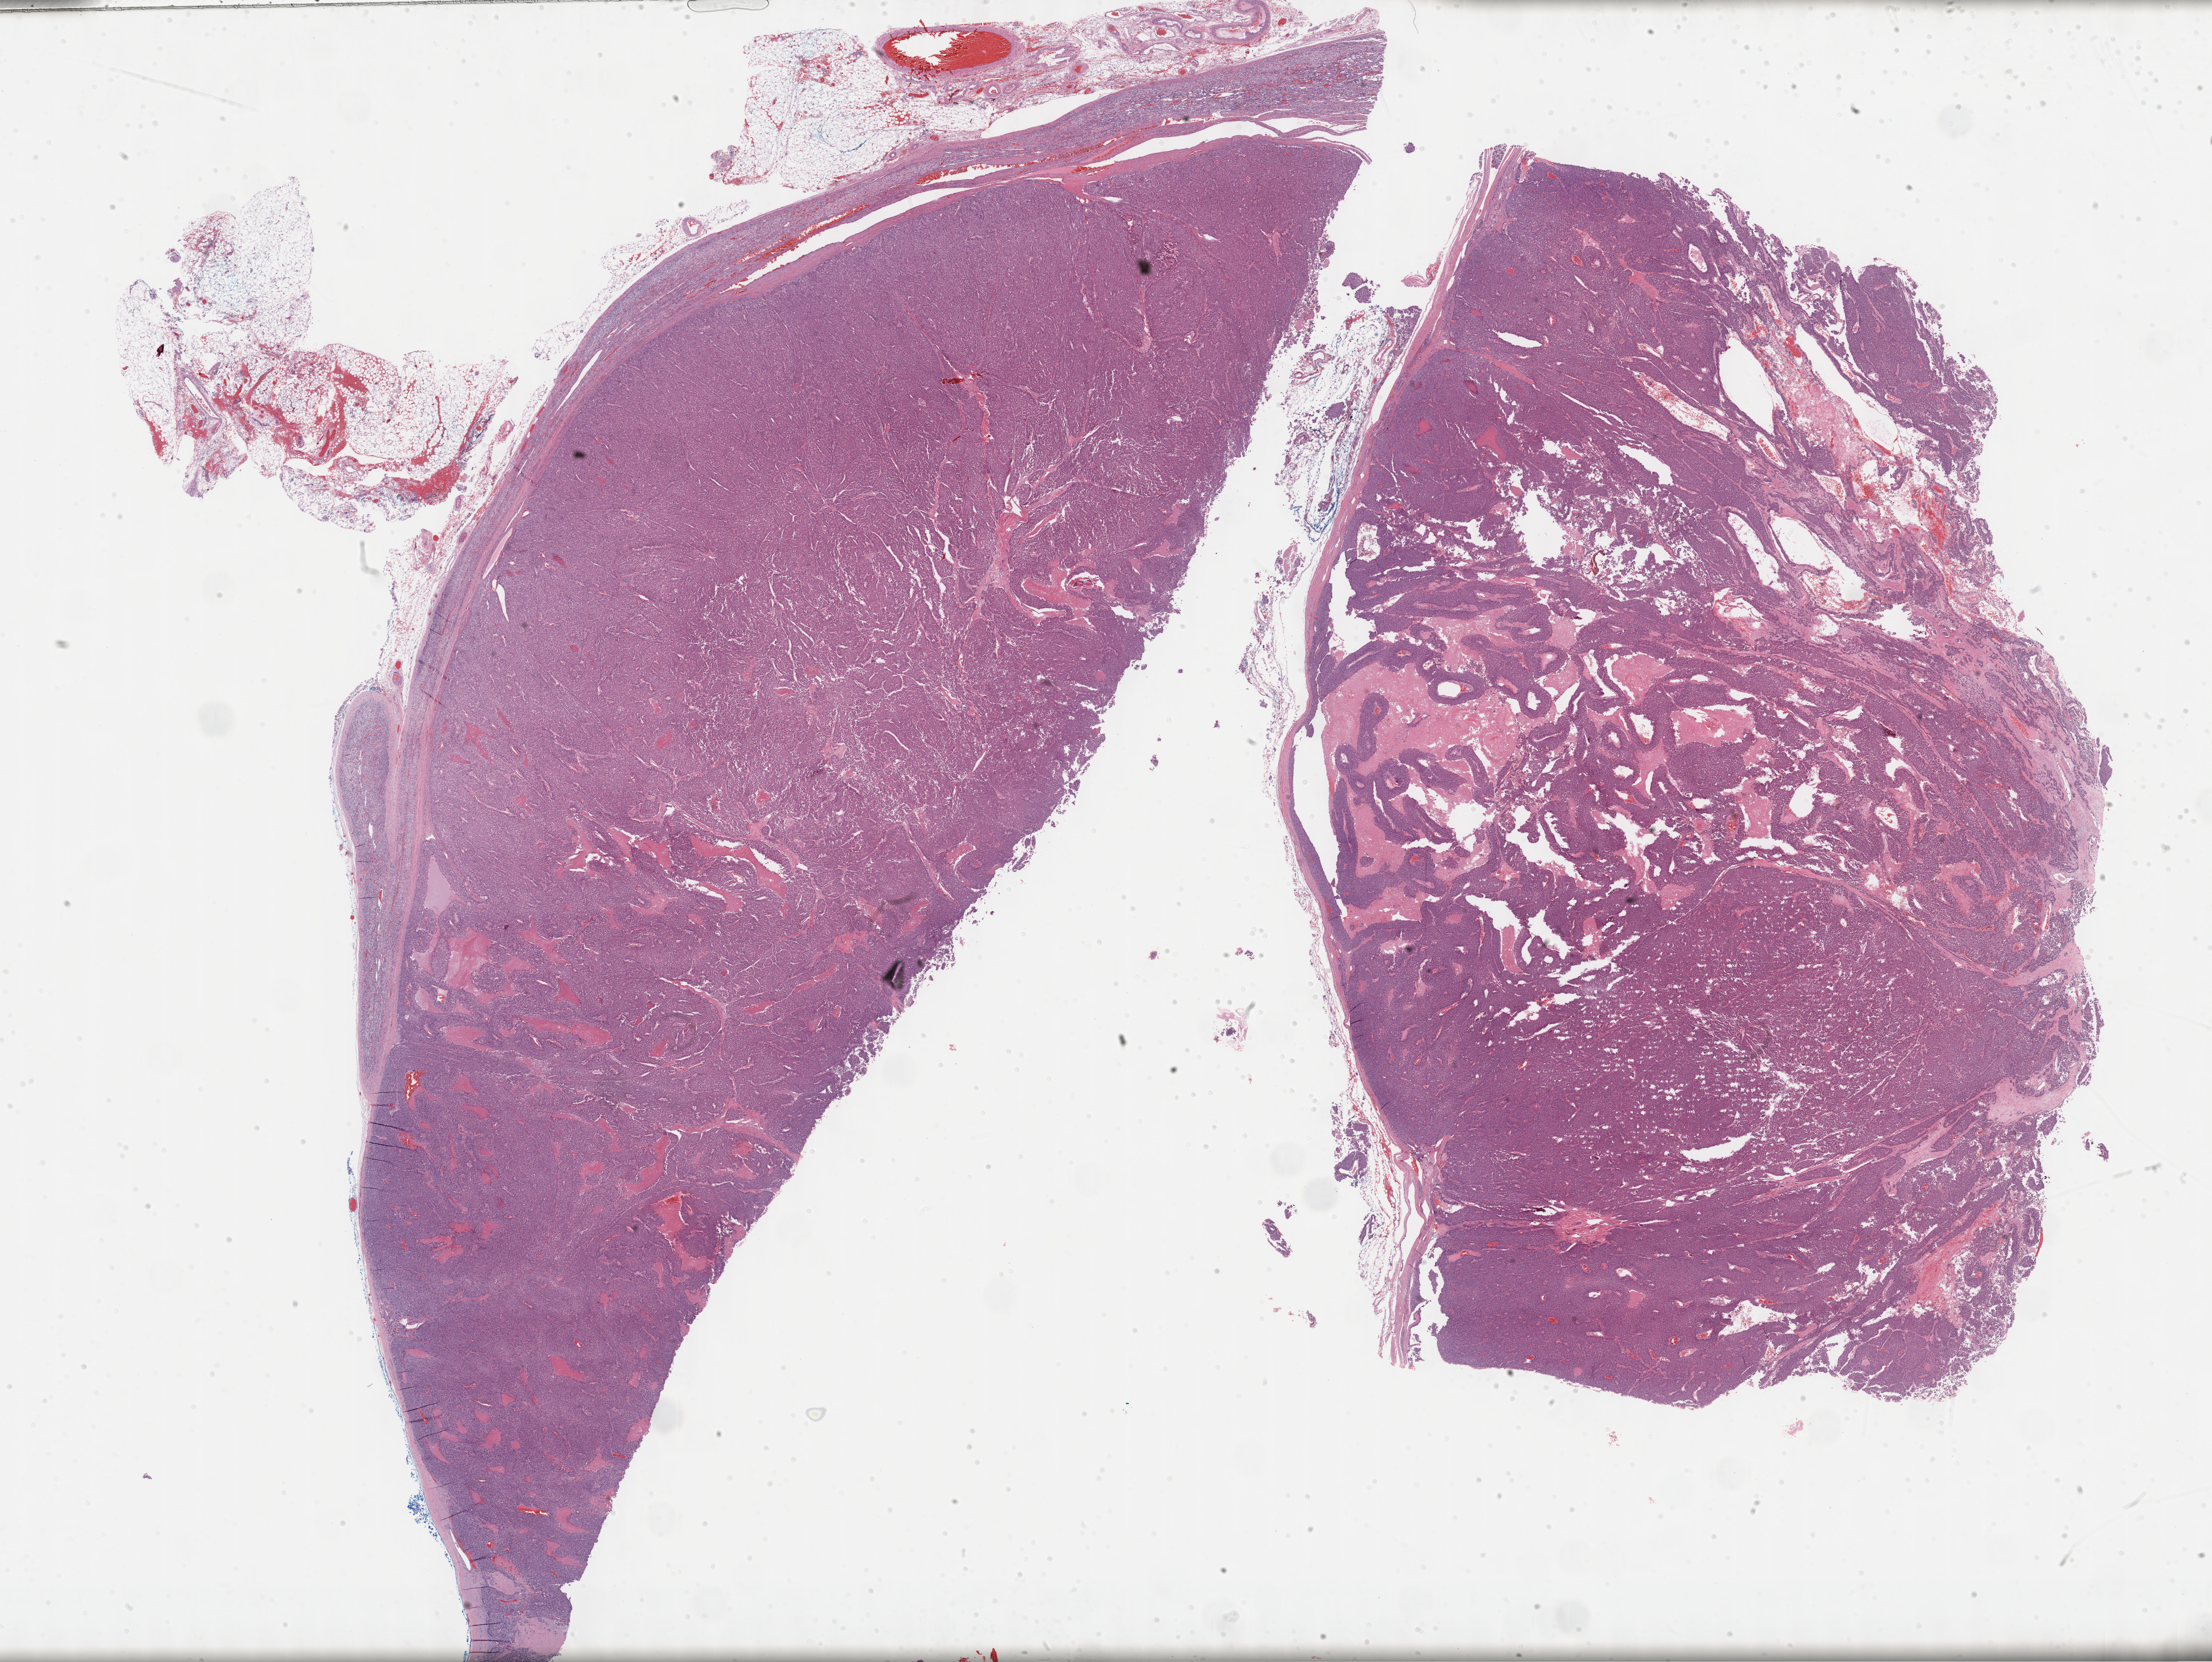
Digitized H&E-stained tissue section (whole slide) — whole scanned area (about 31.2 x 23.5 mm, acquisition: 40x scan) shown as a low-resolution overview, formalin-fixed paraffin-embedded (FFPE) diagnostic section, adrenal cortex, primary tumour sample. Female patient; age at initial diagnosis 69 years.
Pathologic diagnosis: Adrenal cortical carcinoma (cortex of adrenal gland). Laterality: left.